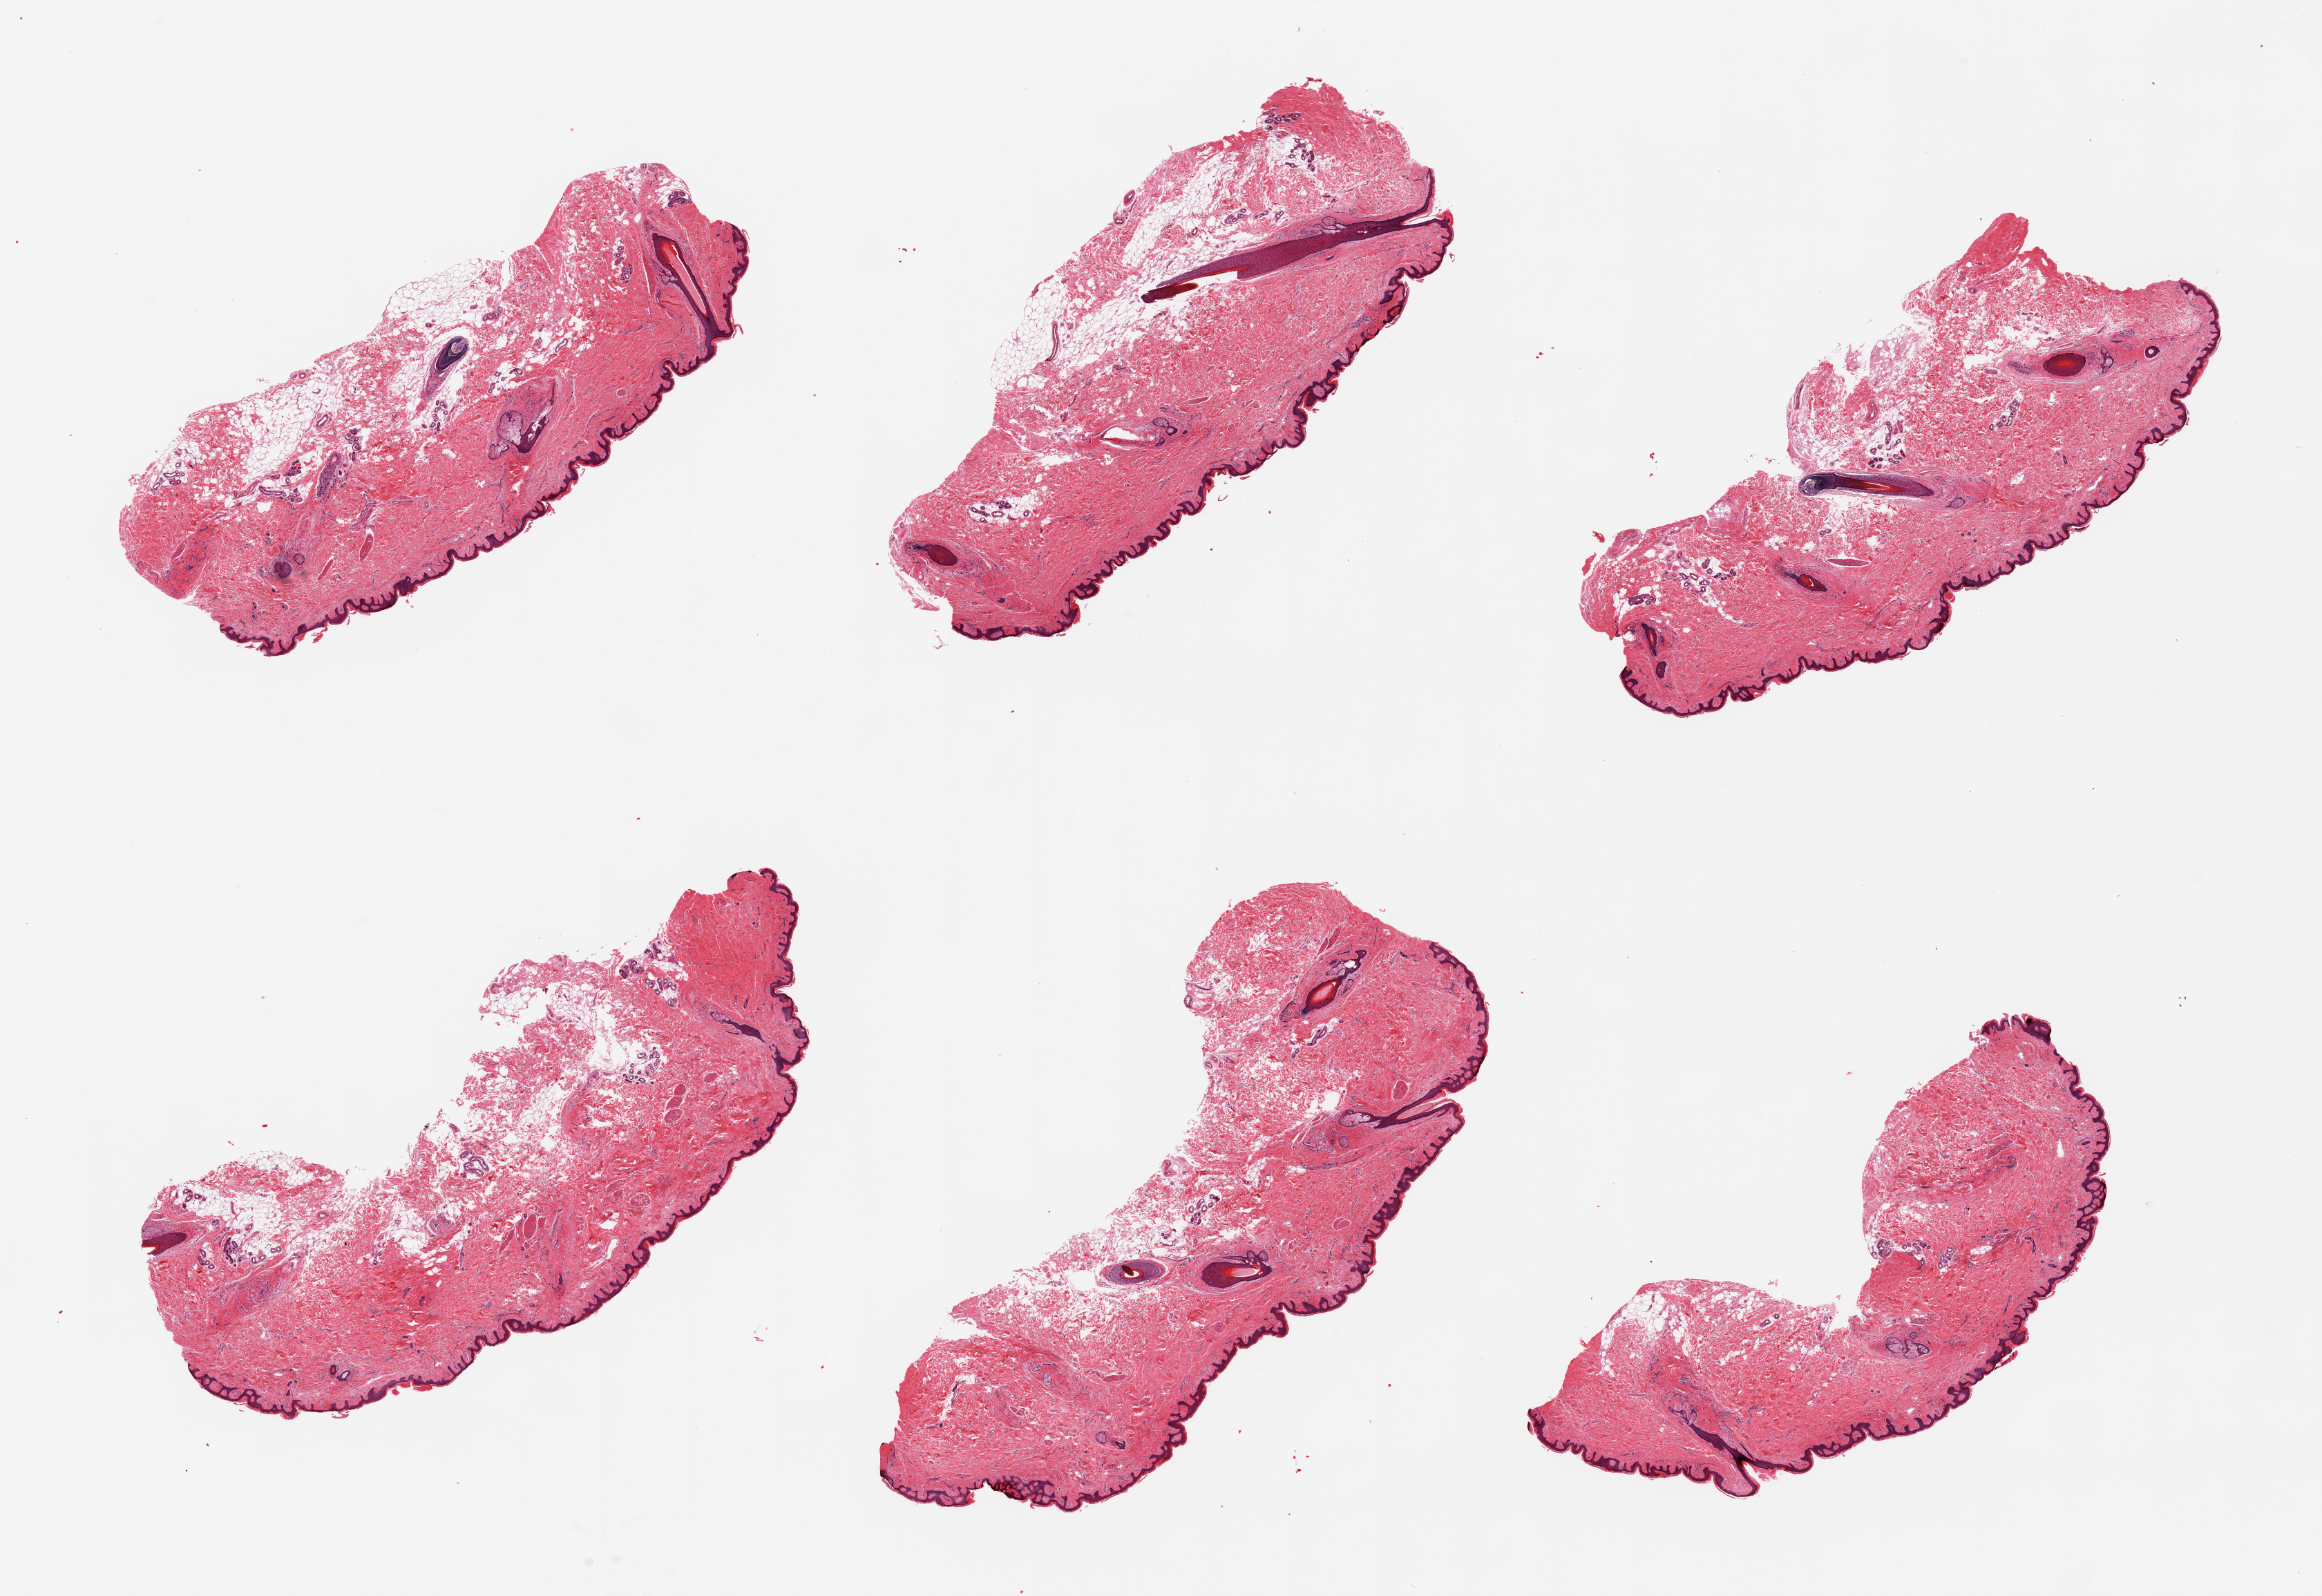
Hematoxylin and eosin (H&E) whole-slide image — shown as a low-resolution overview of the whole scanned area (about 26.6 x 18.3 mm). PAXgene-fixed, paraffin-embedded tissue. Target tissue: skin of suprapubic region. Tissue donor sample. Donor: female.
Review note (as recorded): 6 pieces, minimal dermal fat; squamous epithelium is ~45-50 microns.